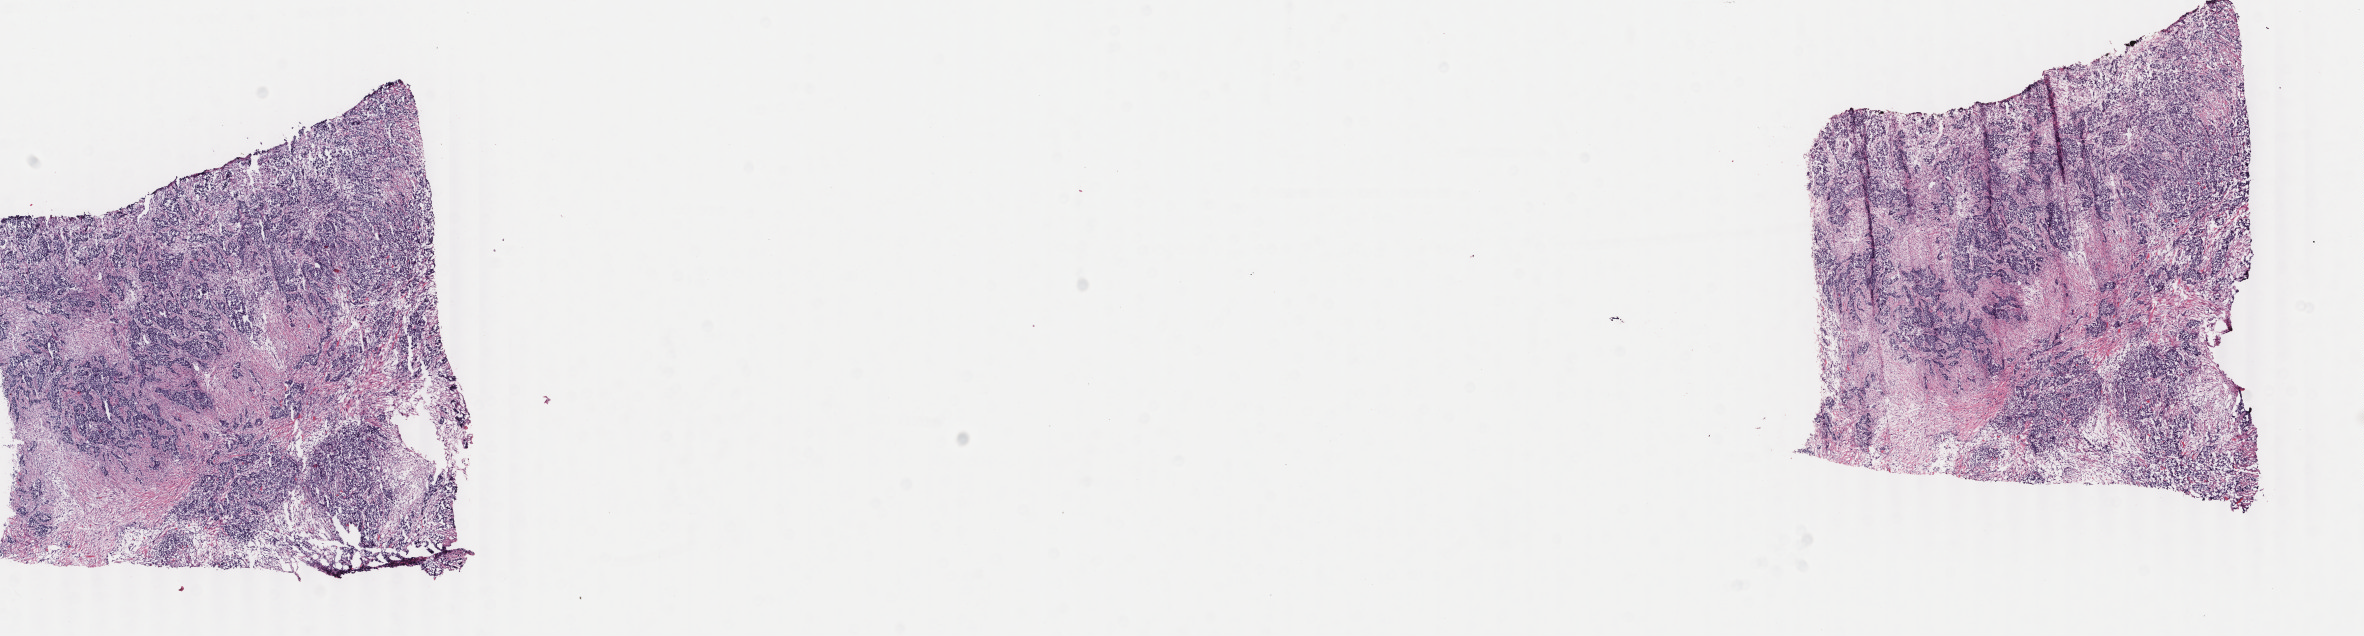
Whole-slide histology image, H&E-stained — a low-resolution overview of the entire scanned area, about 18.8 x 5.1 mm (acquisition: 40x scan). Frozen section from the top of the tissue portion. Breast, primary tumour sample. Female, age 53 years at initial diagnosis.
Diagnosis: Infiltrating duct carcinoma, NOS.